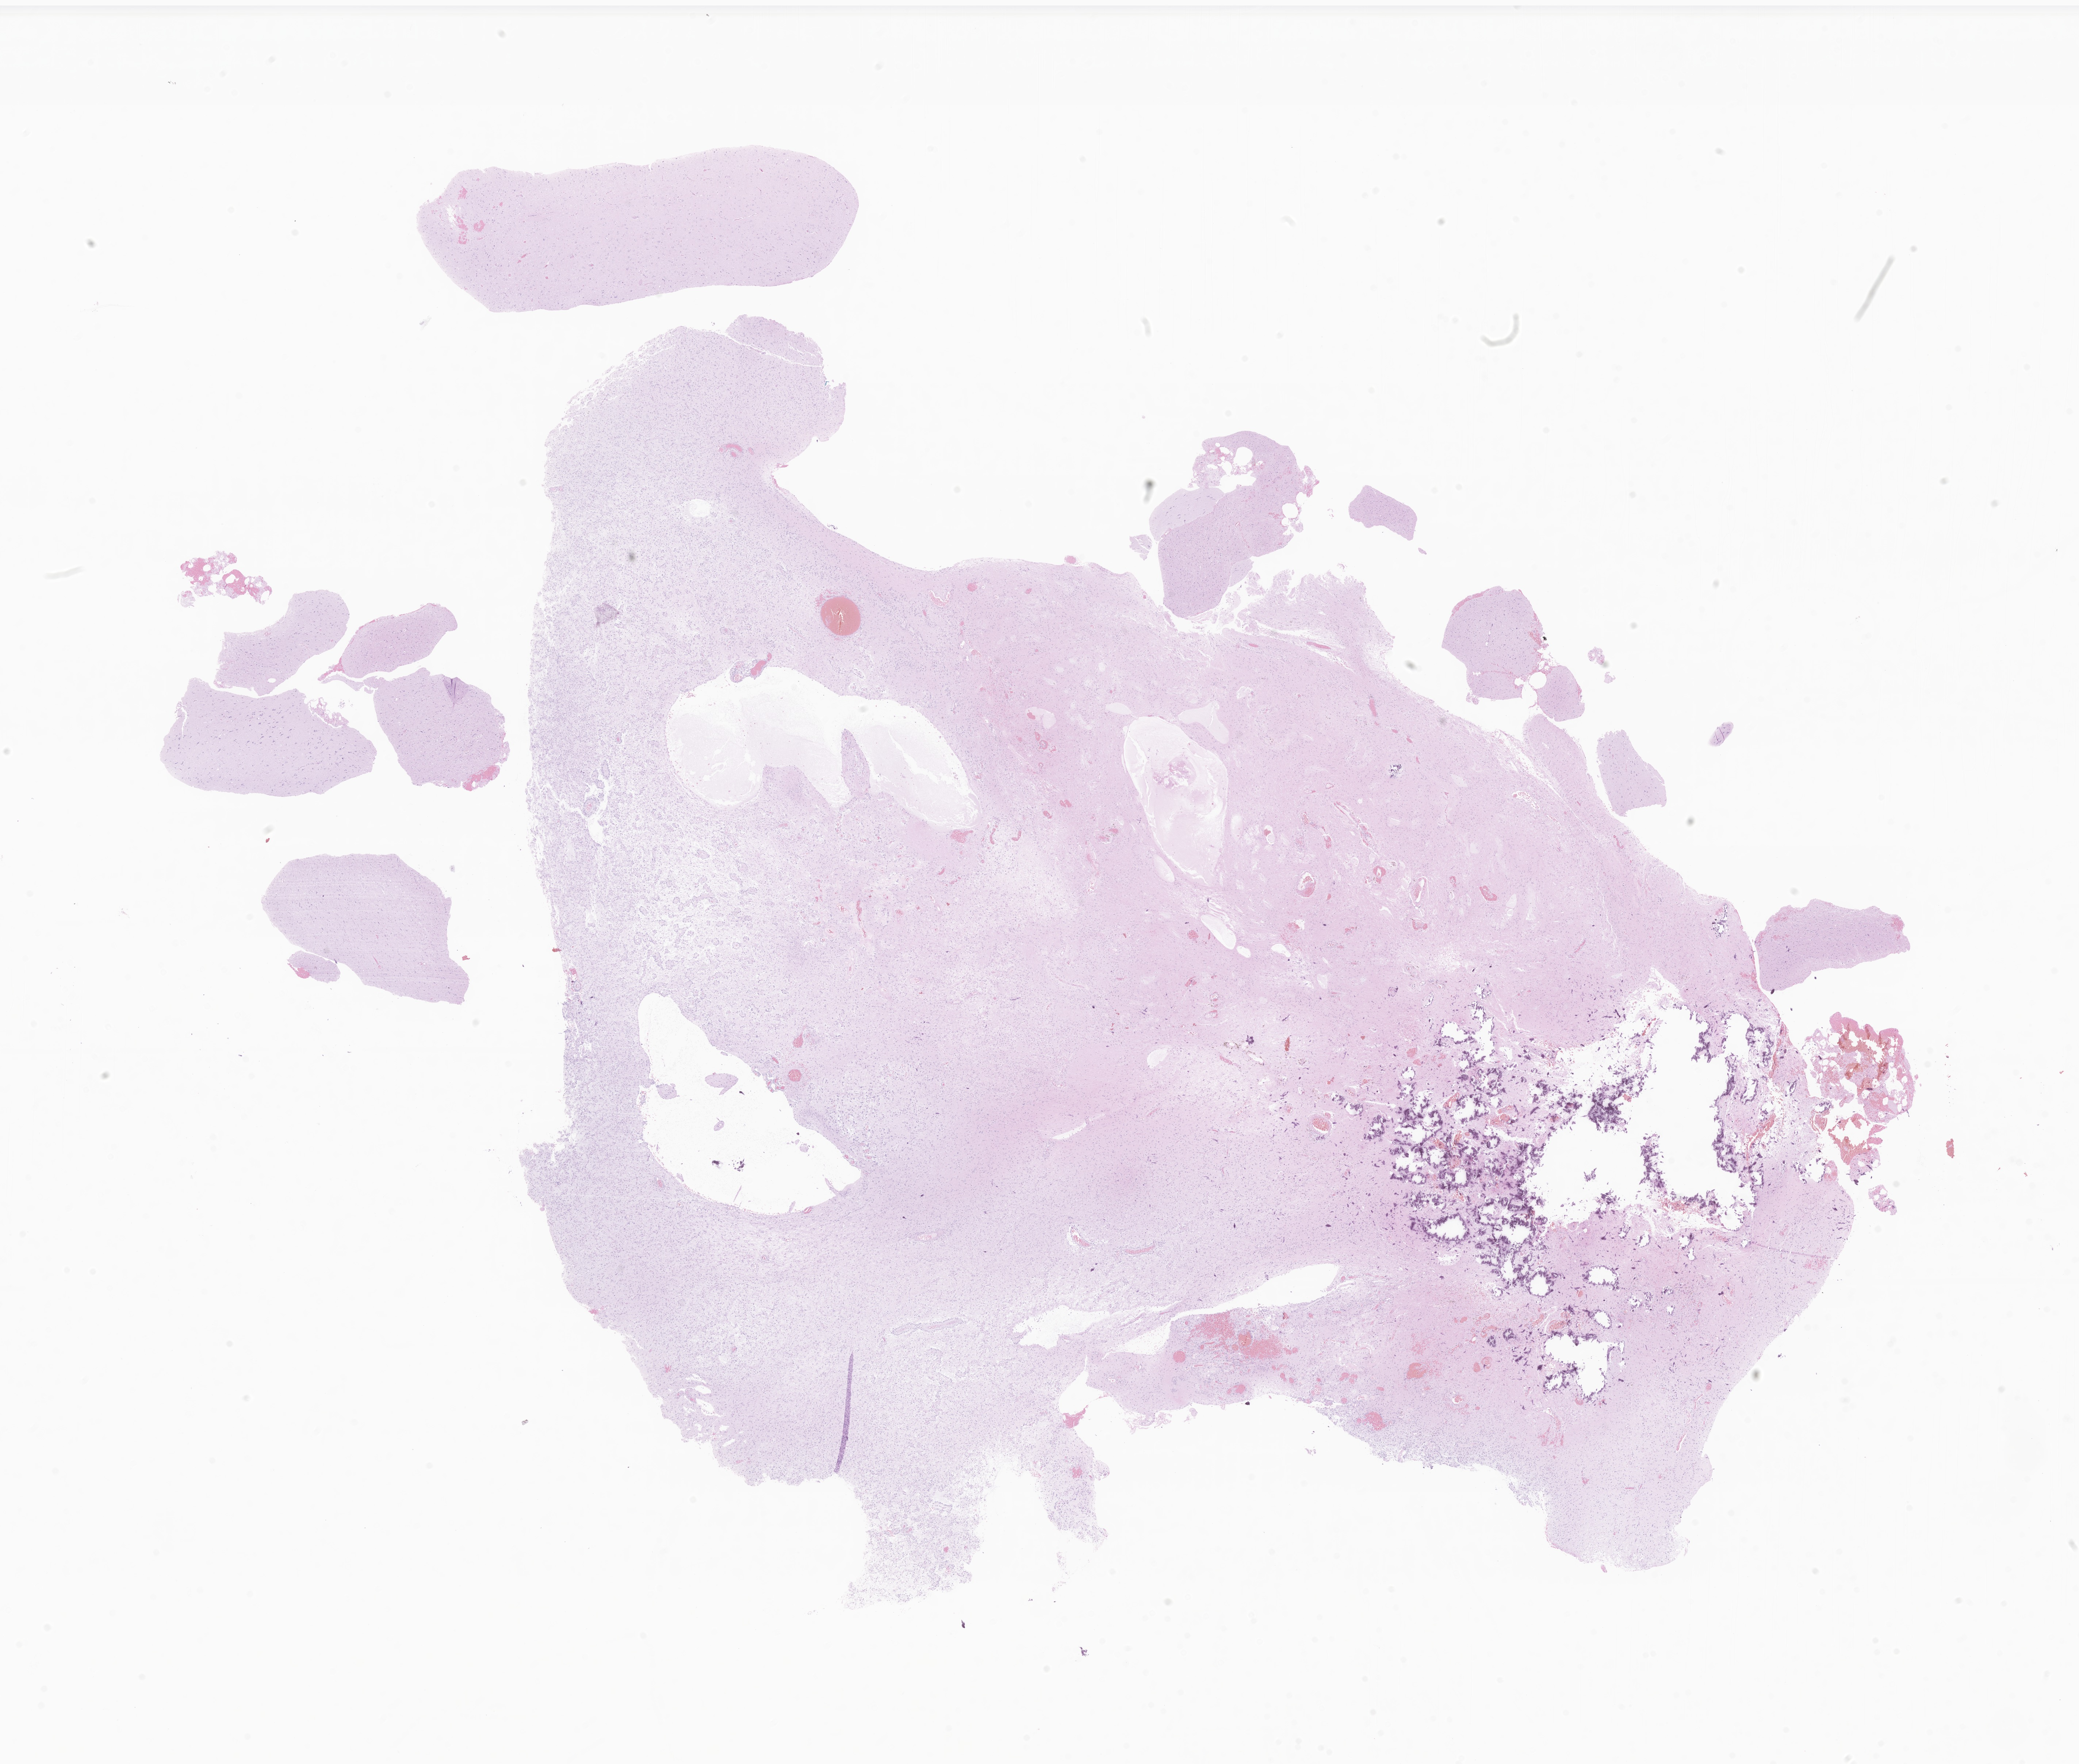
H&E whole-slide image of tumor tissue from the brain, low-resolution overview of the scanned area, about 24.0 x 20.4 mm; formalin-fixed, paraffin-embedded (FFPE) tissue. Male patient, age 227 months (18 years 11 months).
Recorded diagnosis: Ganglioglioma, NOS.